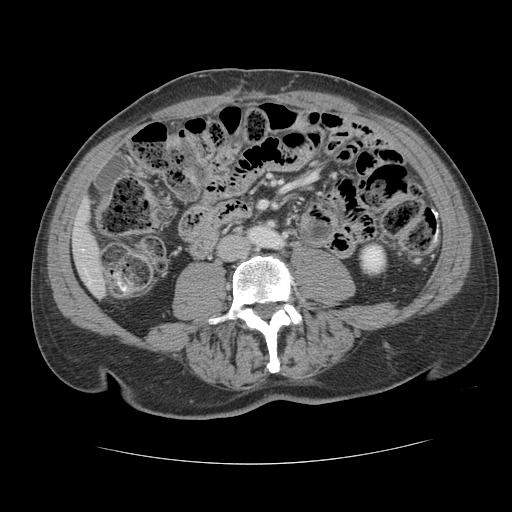
Contrast-enhanced abdominal CT, one axial slice. Position 23 of 134 along the scan axis. Reconstruction kernel STANDARD. Intravenous contrast given. Soft-tissue window (W 400 / L 40 HU). 2.5 mm slice thickness. 512 × 512 image matrix, field of view 377 × 377 mm. Male patient, age 68 years. From the clinical record (not read from this slice): diagnosis: colorectal cancer liver metastases, imaged before liver resection; multiple liver metastases: yes.
Annotated regions visible in this slice (expert manual segmentation):
- liver: bounding box [x1, y1, x2, y2] px = [73, 207, 105, 295]
- planned liver remnant (the part of the liver to remain after resection): [73, 208, 105, 295]